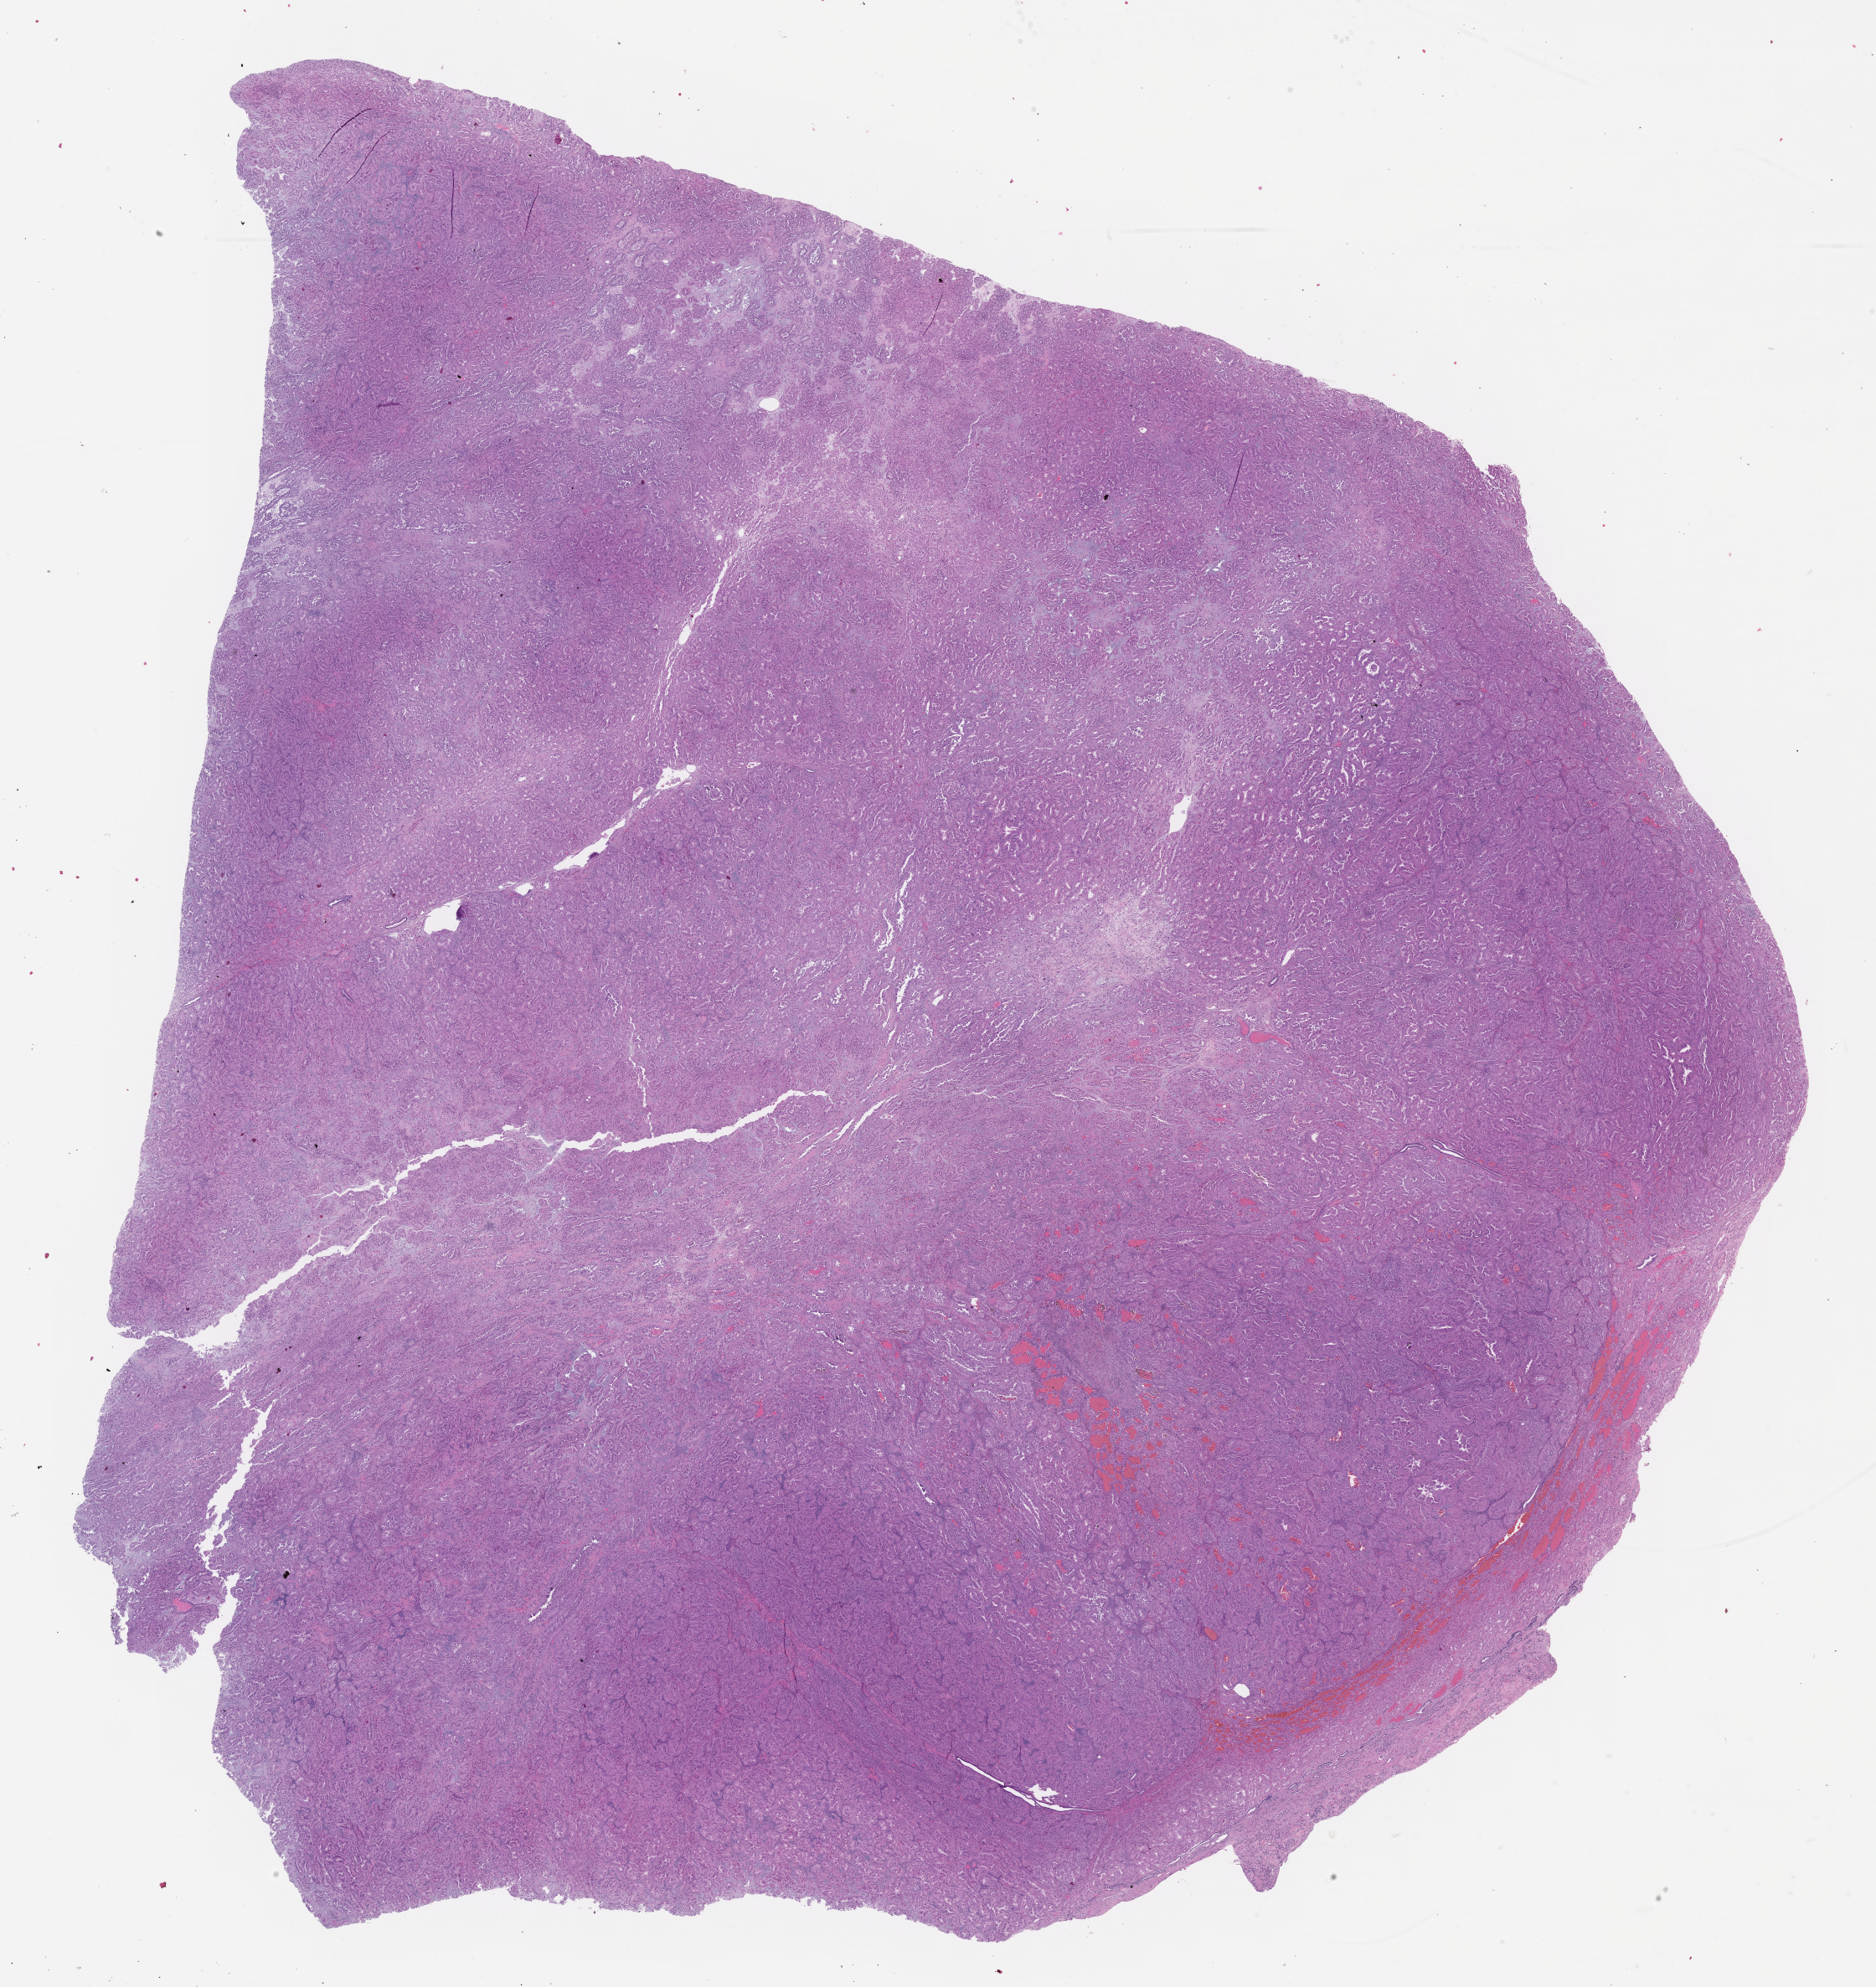
Digitized H&E tissue section (whole slide), shown as a low-resolution overview of the whole scanned area (about 18.1 x 19.2 mm, from a 40x scan), FFPE section, primary tumour sample from the kidney. Male patient; age at initial diagnosis 69 years.
AJCC pathologic stage: I (7th edition). Laterality: right. Histologic diagnosis: Papillary adenocarcinoma, NOS.